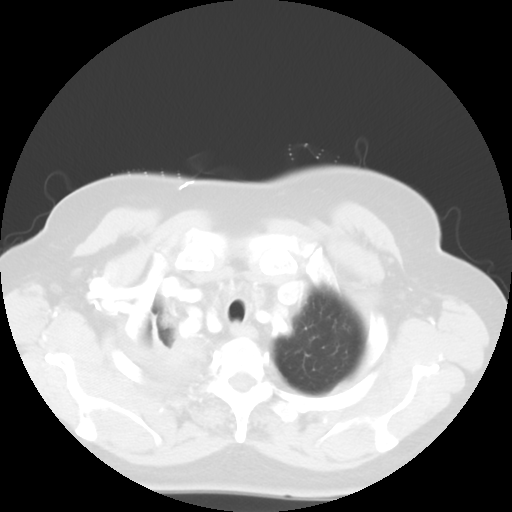
Chest CT, one axial slice. Position 47 of 52 along the scan axis. Lung window (W 1500 / L -600 HU). 5 mm slice thickness. 512 × 512 image matrix, field of view 333 × 333 mm. Patient: female, 81 years. Case-level facts recorded for this patient, not image findings: clinical TNM (as recorded): T4 N3 M1b.
Structures marked on this image (bounding box drawn by a radiologist):
- lung tumour (recorded histology: adenocarcinoma): box from (x=148, y=312) to (x=207, y=378) px